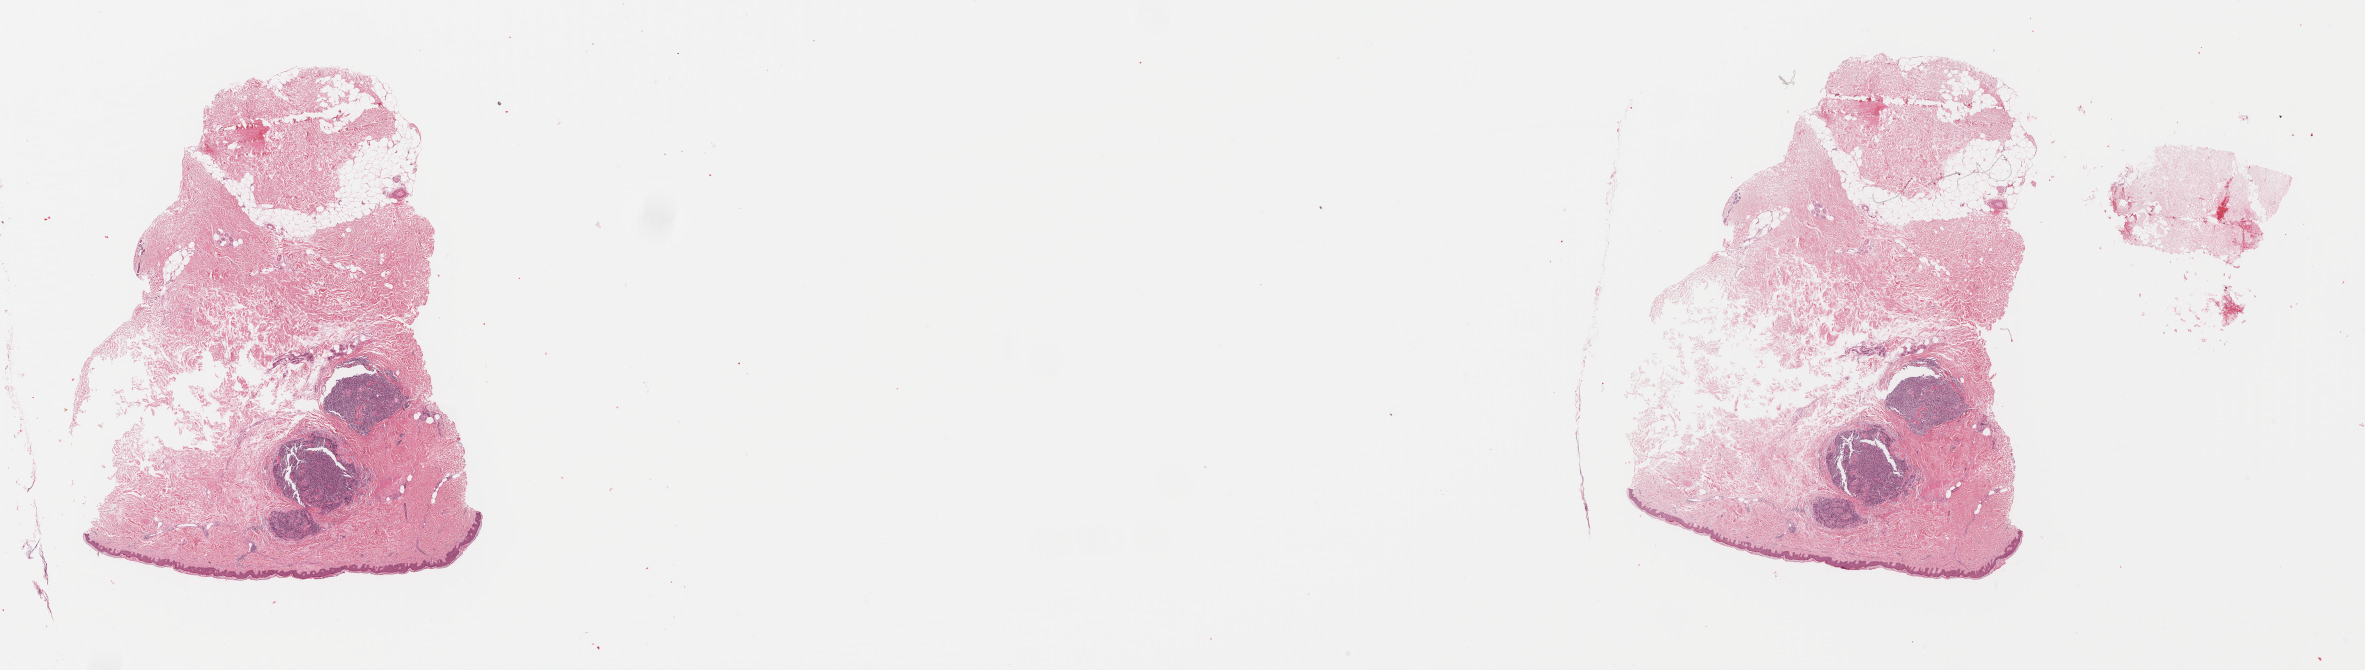
Whole-slide histology image, Hematoxylin and eosin (H&E) stained — whole scanned area (about 37.2 x 10.5 mm) shown as a low-resolution overview, FFPE section, metastatic tumour sample, sampled site: skin. Female patient; age at initial diagnosis 70 years.
This section: metastatic tumour tissue. Patient diagnosis: Malignant melanoma, NOS.